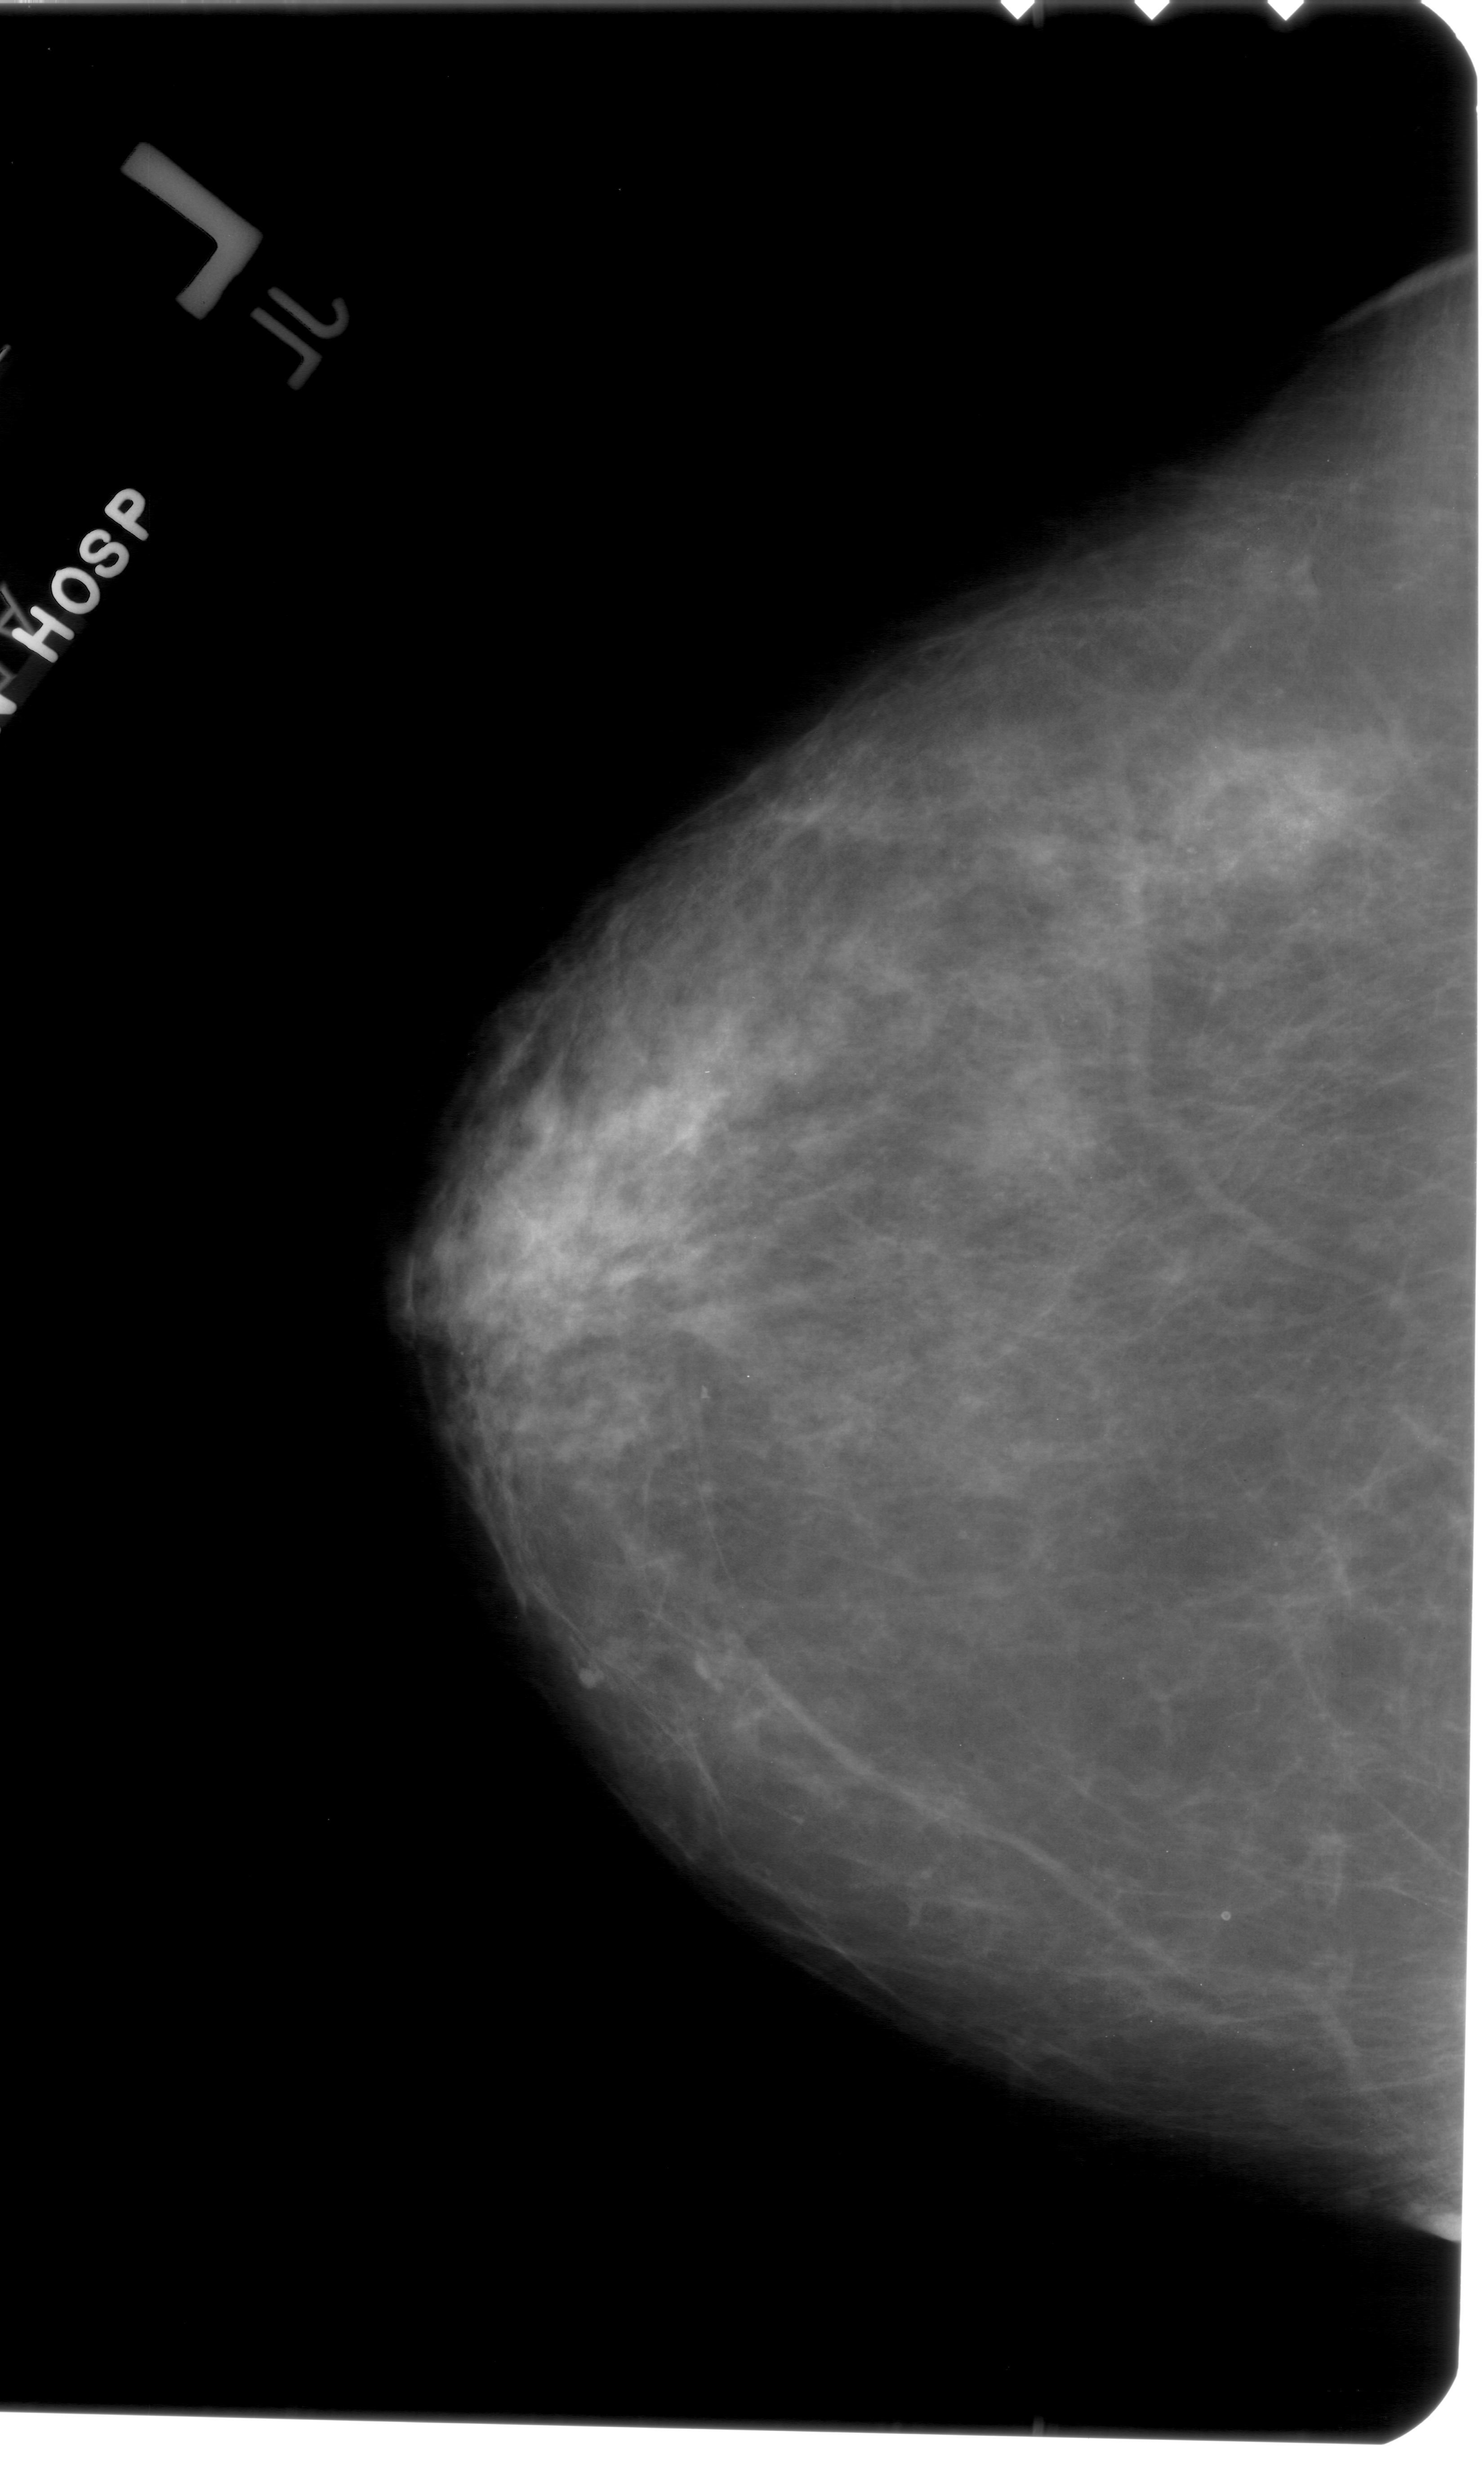
Scanned film-screen mammogram; left breast; craniocaudal (CC) view; BI-RADS breast density category 3 (scale 1–4); 1484 × 2469 image matrix.
Expert-marked regions of interest on this image (one box per marked abnormality):
- calcifications, morphology amorphous, distribution clustered; BI-RADS assessment category 4; pathology result (as recorded, not read from the image): benign: bounding box (x1, y1, x2, y2) in pixels: (1148, 645, 1391, 956)